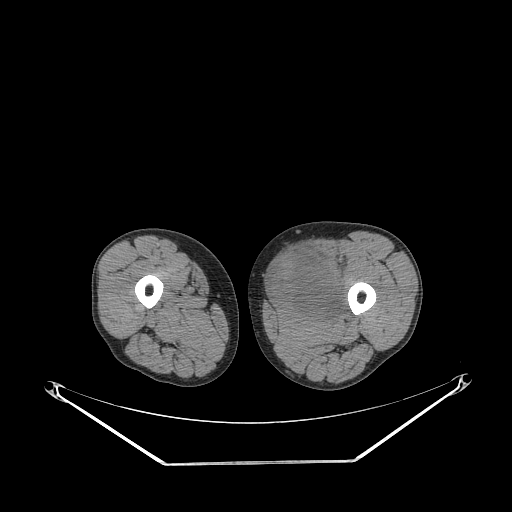
CT of an extremity soft-tissue mass (from a PET/CT study), one axial slice. Slice 235 of 267 in the series (ordered by position). Reconstruction kernel STANDARD. Soft-tissue window (W 400 / L 40 HU). 3.75 mm slice thickness. 512 × 512 image matrix, field of view 500 × 500 mm. Male patient. Case-level facts recorded for this patient, not image findings: histological type: pleiomorphic liposarcoma; grade: high; site of the primary tumour: left thigh.
Outlined on this slice (expert contour drawn on MRI and transferred to this co-registered scan by the dataset authors):
- gross tumour volume including surrounding oedema: bounding box <270,240,350,321> (left, top, right, bottom; pixels)
- gross tumour volume (mass): <270,251,341,316>